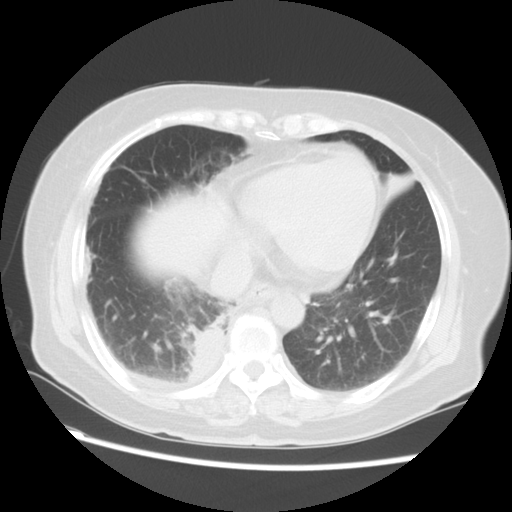
Chest CT, one axial slice; position 22 of 57 along the scan axis; 120 kVp; lung window (W 1500 / L -600 HU); 5 mm slice thickness; 512 × 512 image matrix, field of view 350 × 350 mm. Female patient, age 69 years. Case-level facts recorded for this patient, not image findings: clinical TNM (as recorded): T2 N1 M1a.
Outlined on this slice (rectangle marked by the reading radiologist):
- lung tumour (recorded histology: adenocarcinoma): box from (x=181, y=320) to (x=230, y=389) px